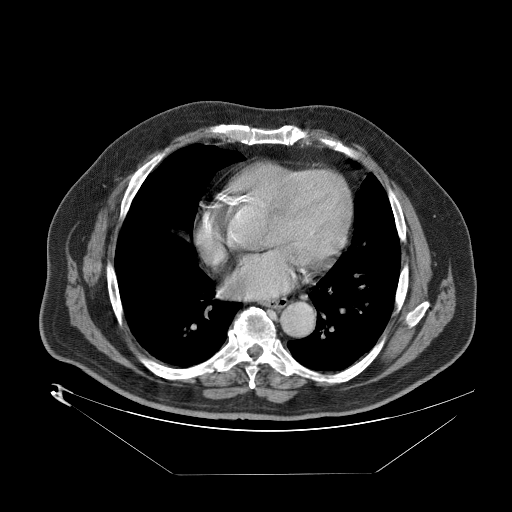
Contrast-enhanced abdominal CT (liver protocol), one axial slice; position 89 of 89 along the scan axis; 140 kVp; one of 2 acquisitions stored at this slice position; soft-tissue window (W 400 / L 40 HU); 2.5 mm slice thickness; 512 × 512 image matrix, field of view 480 × 480 mm. From the clinical record (not read from this slice): diagnosis: hepatocellular carcinoma (patient treated with transarterial chemoembolisation; whether this scan precedes or follows treatment is not stated here); TNM stage (as recorded): Stage-II; Child-Pugh class: B; tumour differentiation: moderately differentiated; tumour nodularity: multinodular.
Structures marked on this image (semi-automatic segmentation, software-assisted and operator-edited):
- abdominal aorta: box from (x=280, y=302) to (x=314, y=337) px